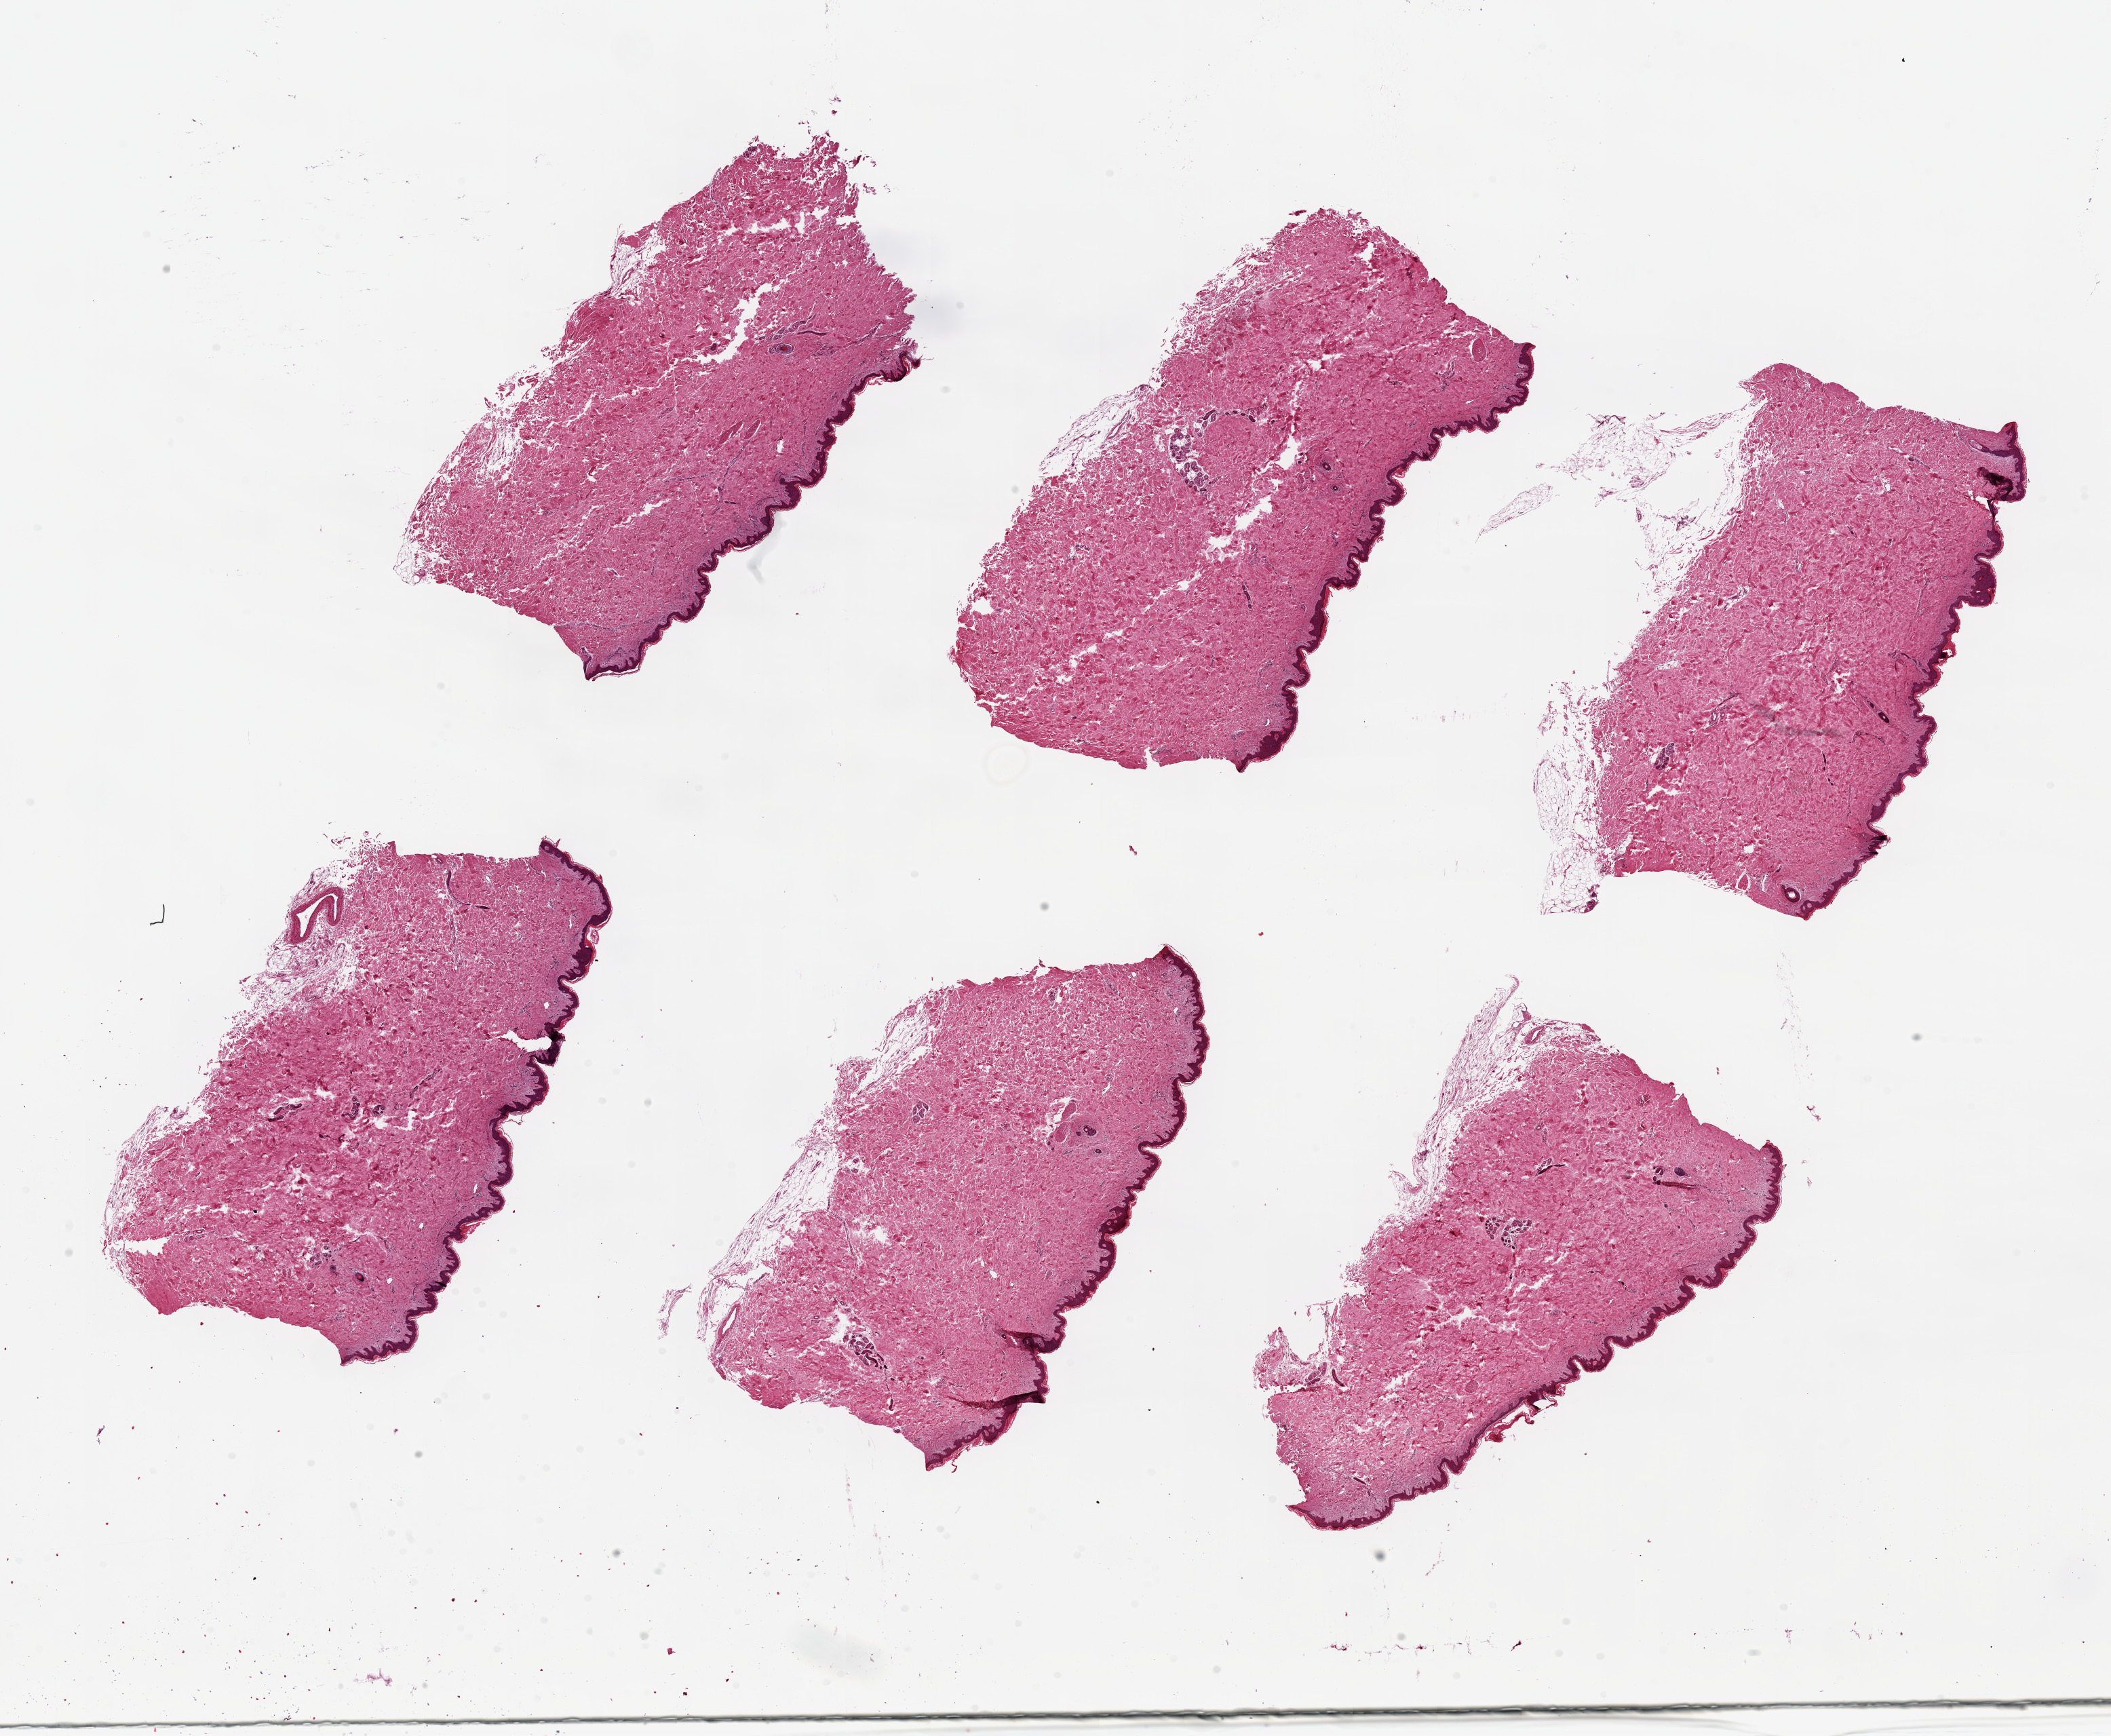
Whole-slide image, H&E stain, brightfield — shown as a low-resolution overview of the whole scanned area (about 24.6 x 20.2 mm); PAXgene-fixed paraffin-embedded (PFPE) section; sampled site (target tissue): skin of suprapubic region; tissue donor sample. Male donor.
* review note (as recorded): 6 pieces ~6x3; squamous epithelium is 2-3% of thickness